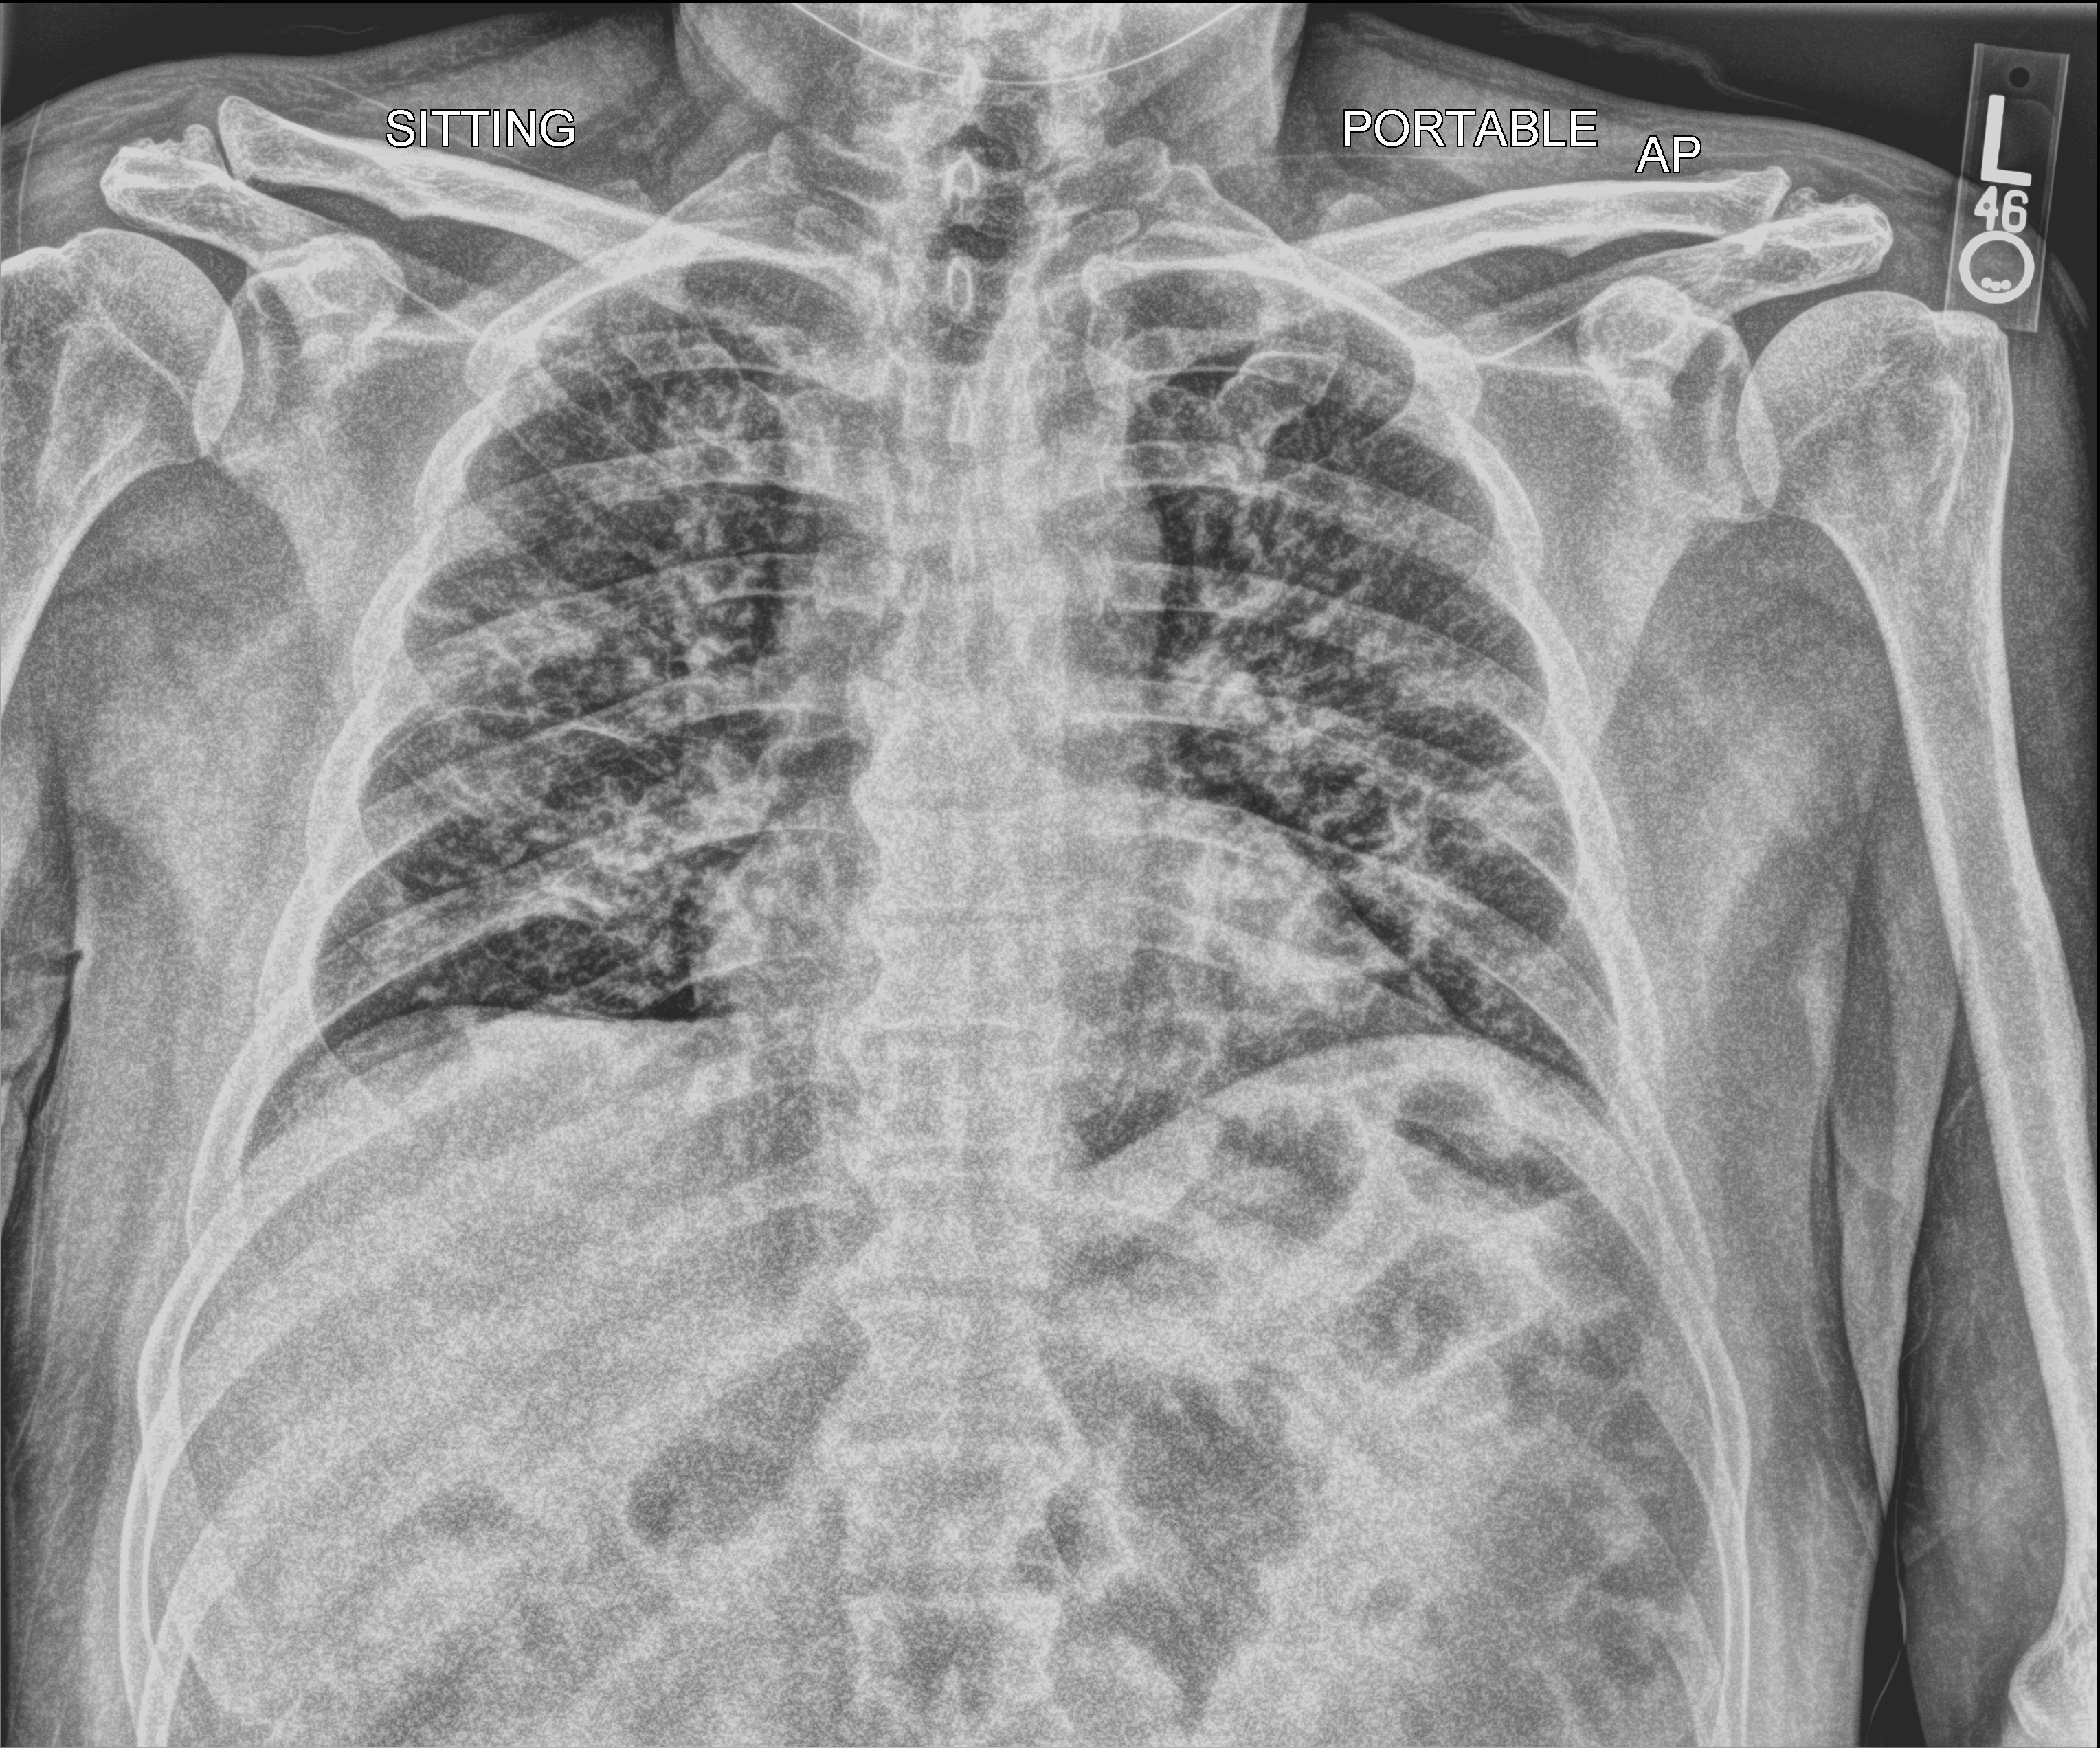
Bedside chest radiograph (computed radiography). Patient hospitalised with COVID-19; male, aged 60–74 years.
From the hospital-stay record, not from the radiograph (when in the stay this image was taken is not recorded):
- other chronic lung disease (admission record): yes
- COPD (admission record): no